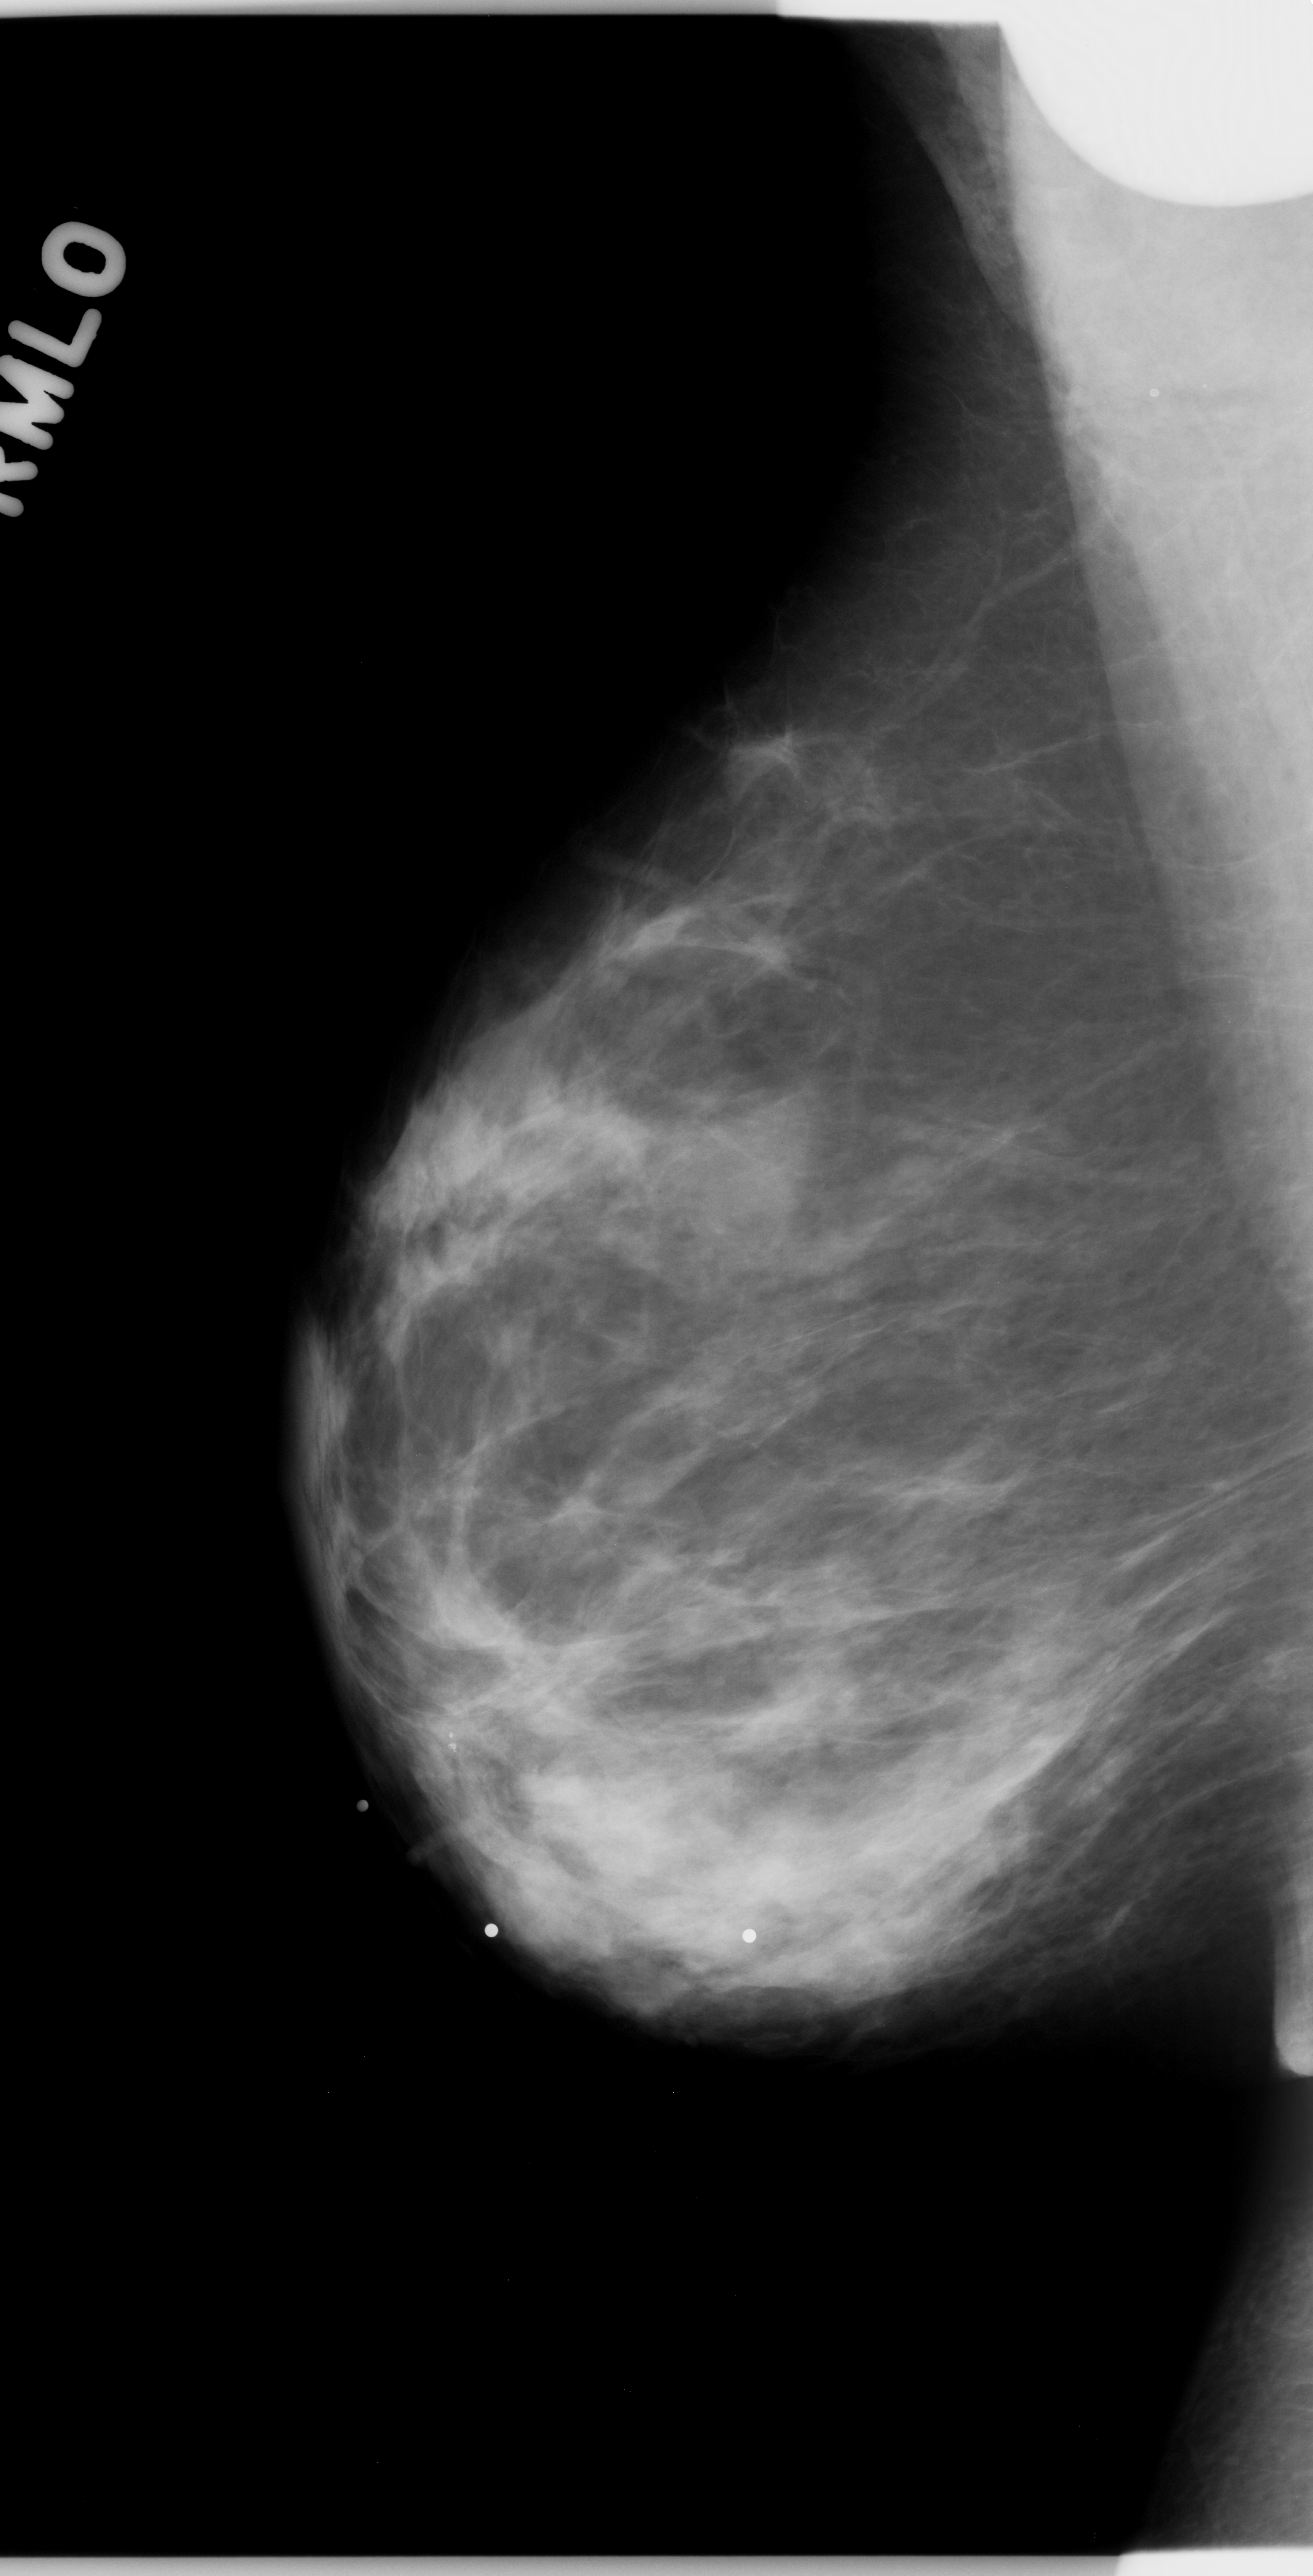
Digitized screen-film mammogram; right breast; MLO view; breast composition: scattered fibroglandular densities (BI-RADS density category 2 of 4).
Finding: mass, shape oval, margins obscured; BI-RADS assessment category 4; pathology (as recorded): malignant.